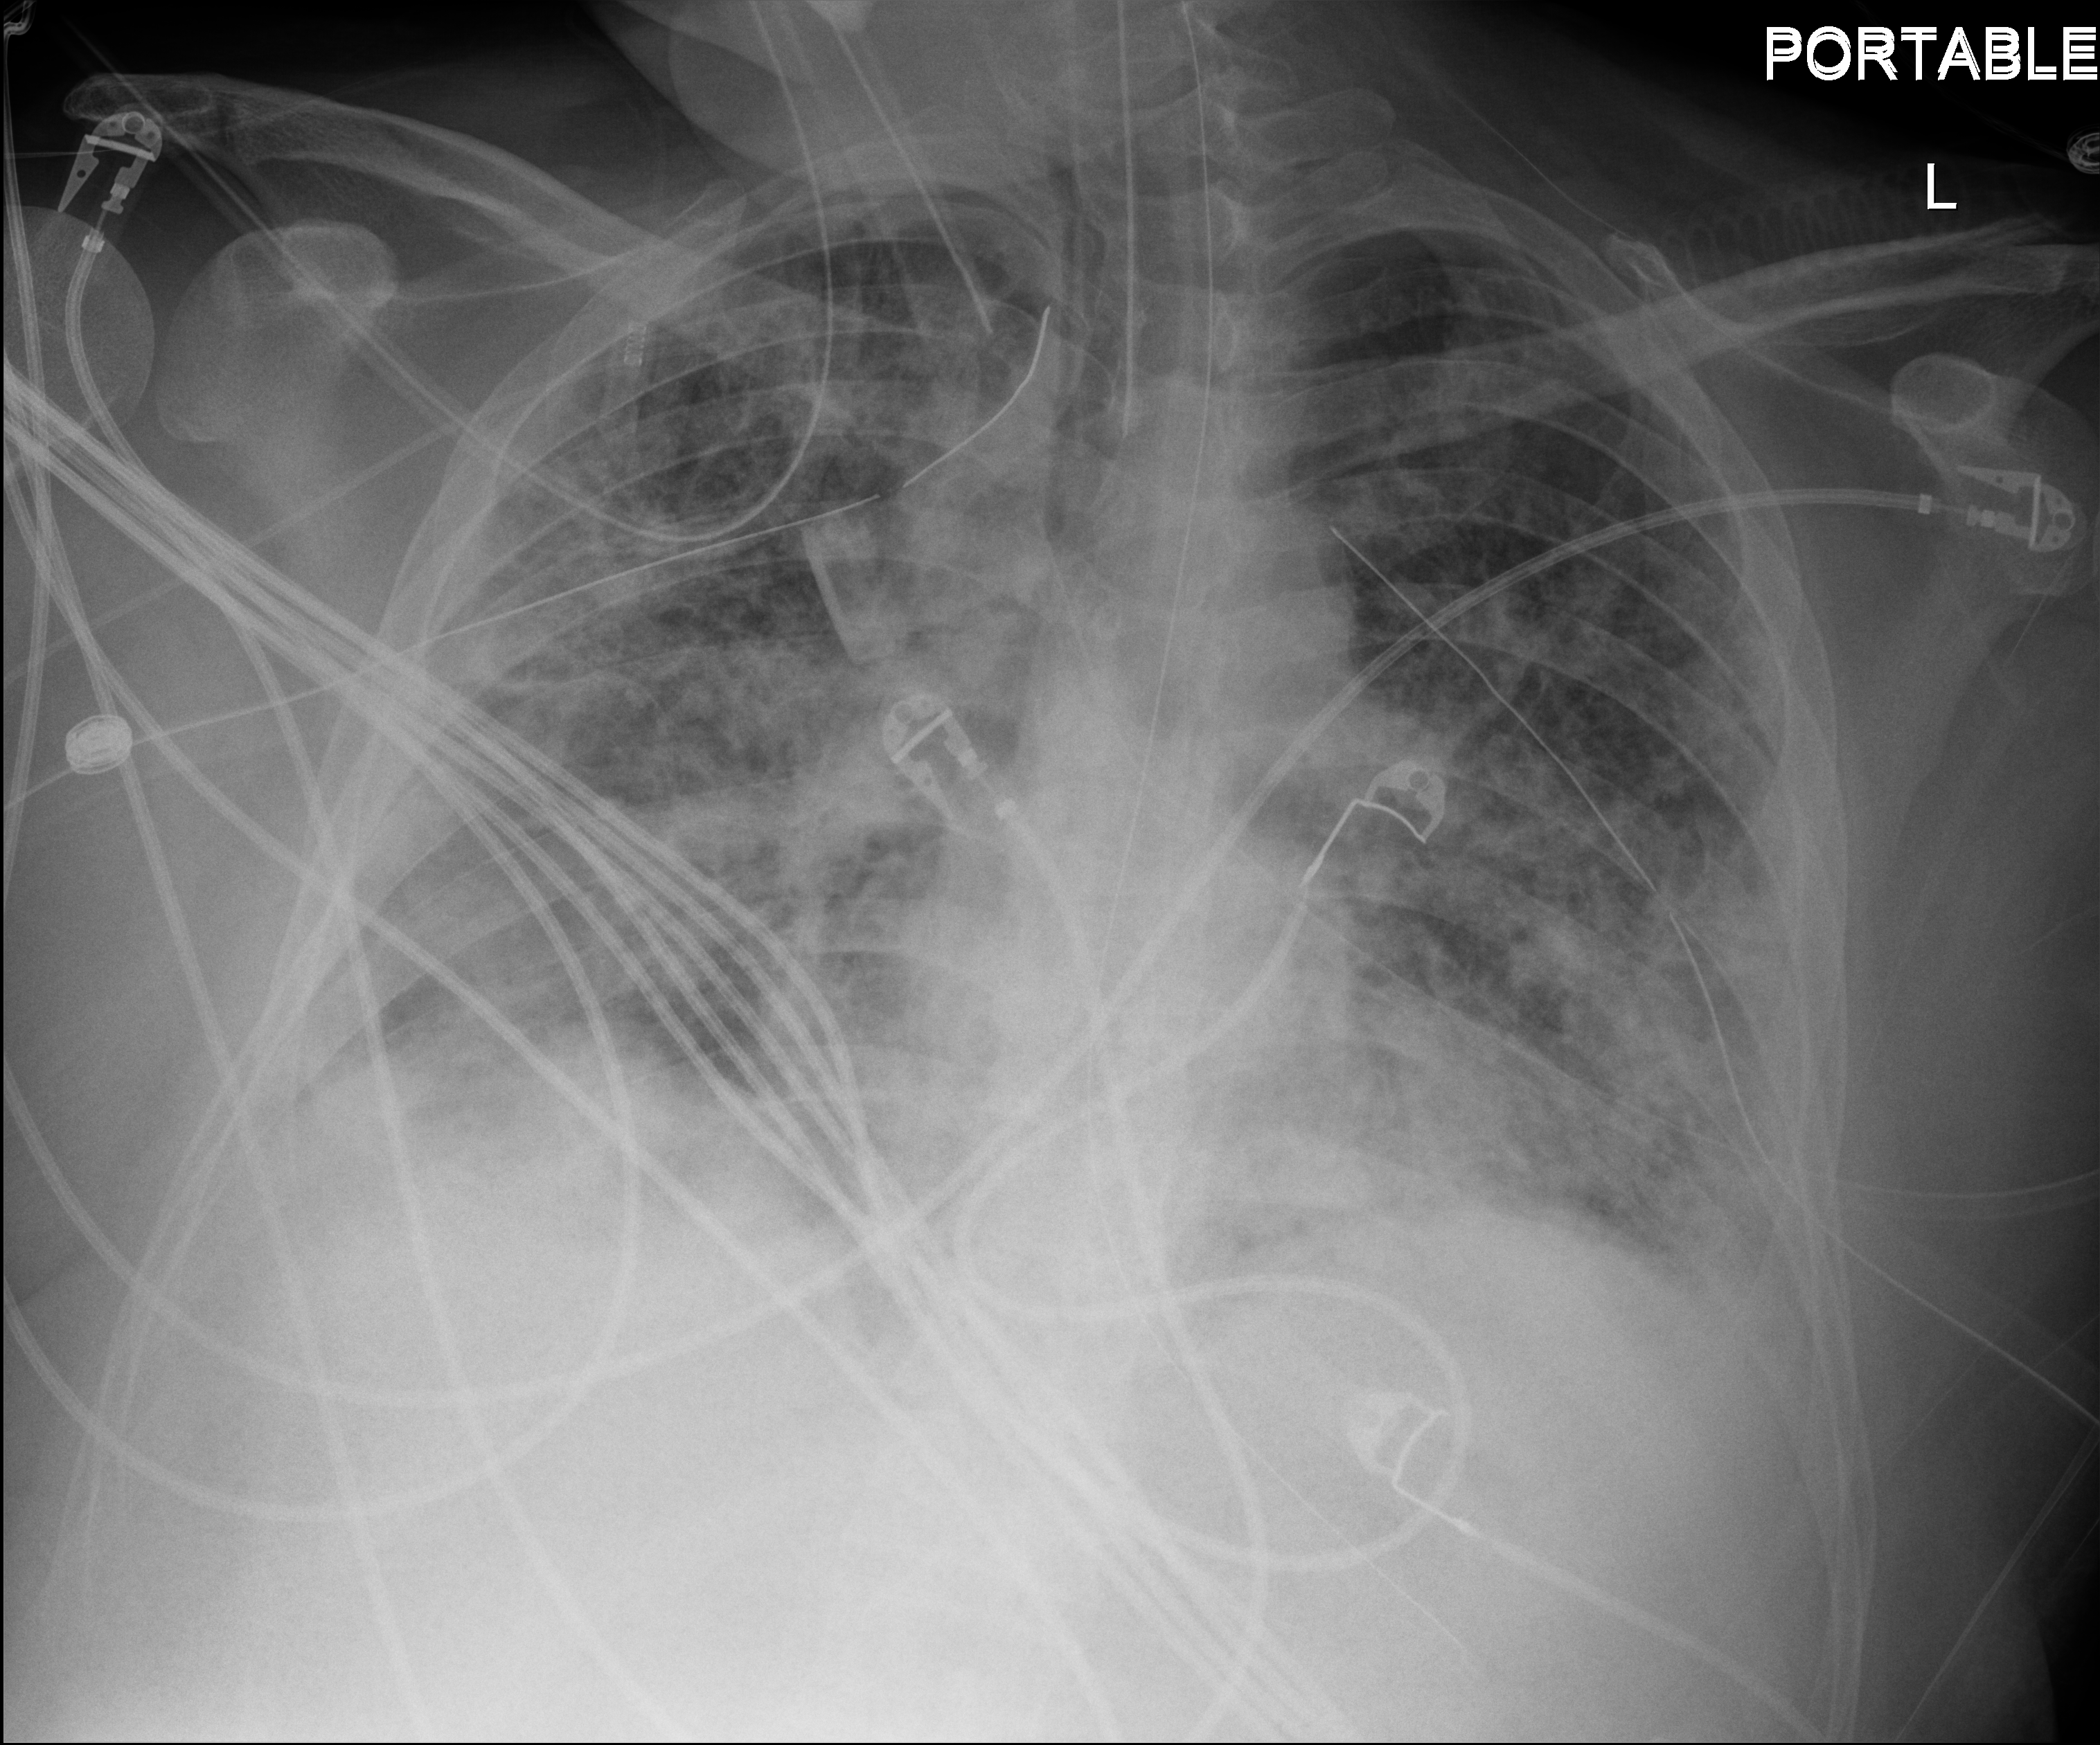
Bedside chest radiograph (digital radiography); anteroposterior (AP) projection. Male patient hospitalised with COVID-19, age 18–59 years.
Hospital-stay facts (about this admission, not read from this image; timing relative to this image not recorded): COPD (admission record): no.